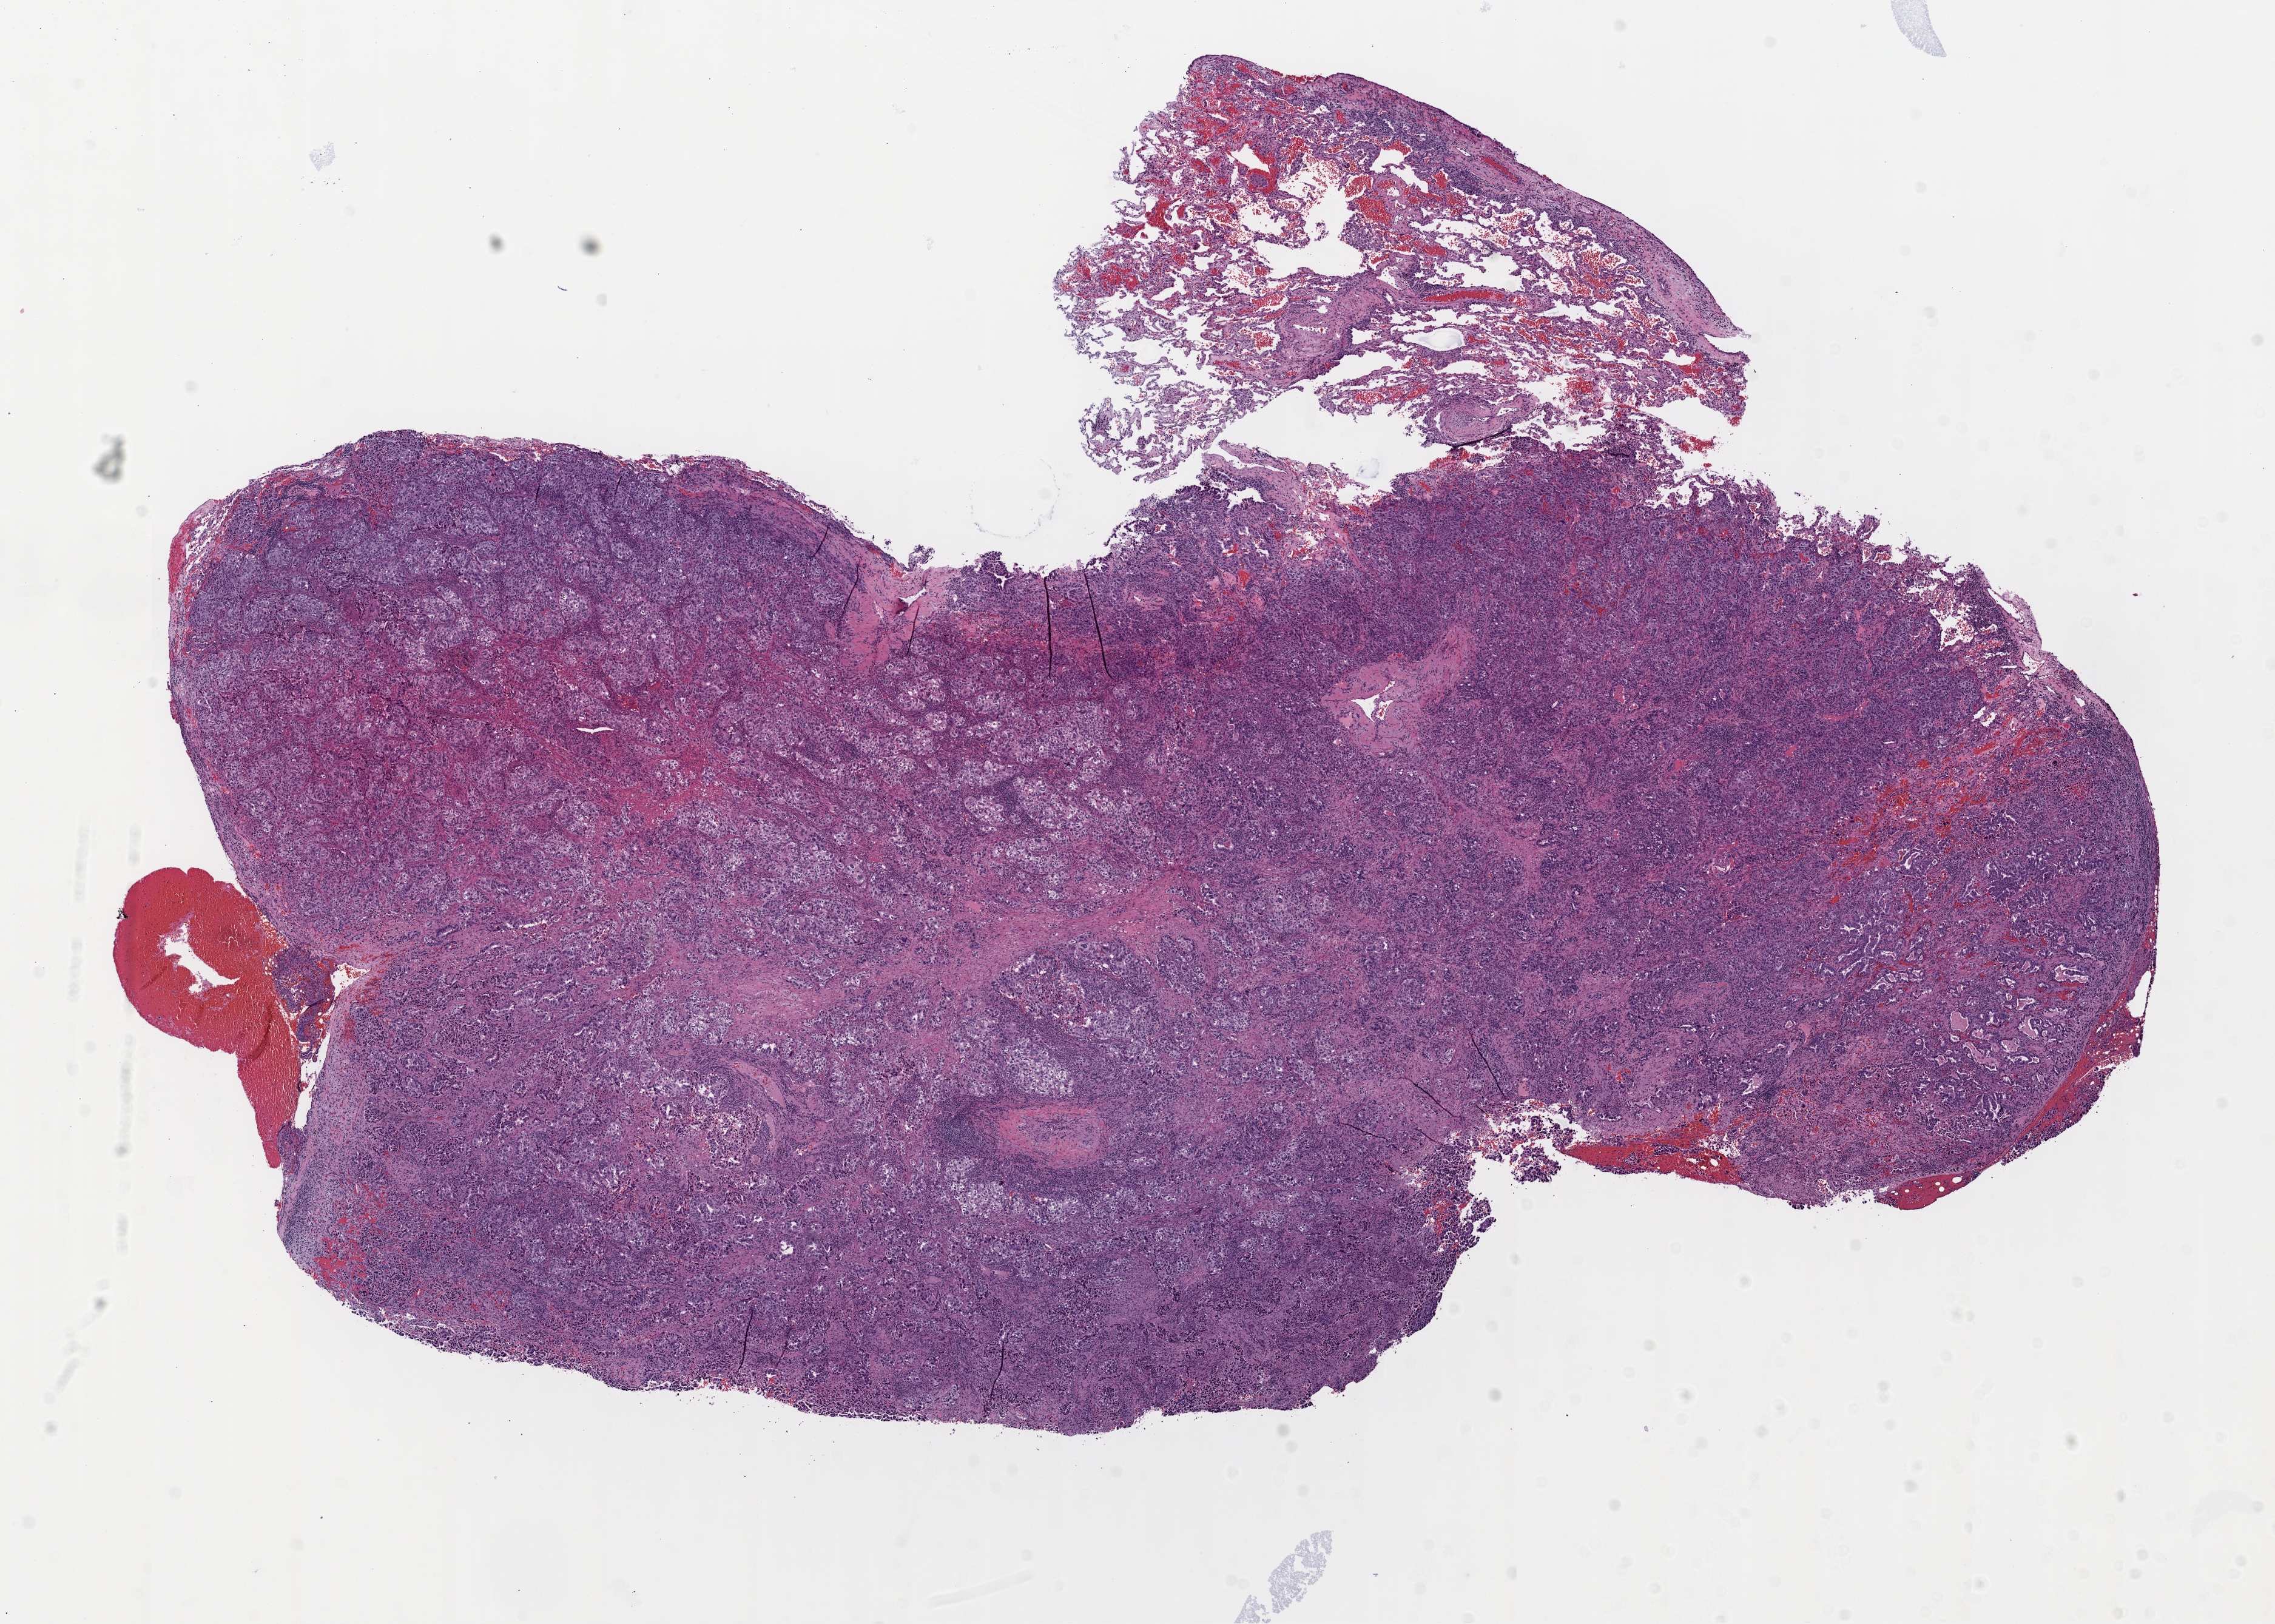
Whole-slide histology image, H&E, whole scanned area (about 15.0 x 10.7 mm) shown as a low-resolution overview; frozen section from the top of the tissue portion; sample: primary tumour, lung. Female, age 60 years at initial diagnosis. Slide review estimates, as recorded: tumour cells 90%, tumour nuclei 75%, stromal cells 9%, necrosis 1%. Inflammatory infiltration, as recorded: lymphocyte infiltration 20%.
Pathologic diagnosis: Adenocarcinoma, NOS (upper lobe, lung). AJCC pathologic stage: IA. TNM: T1 N0 M0.